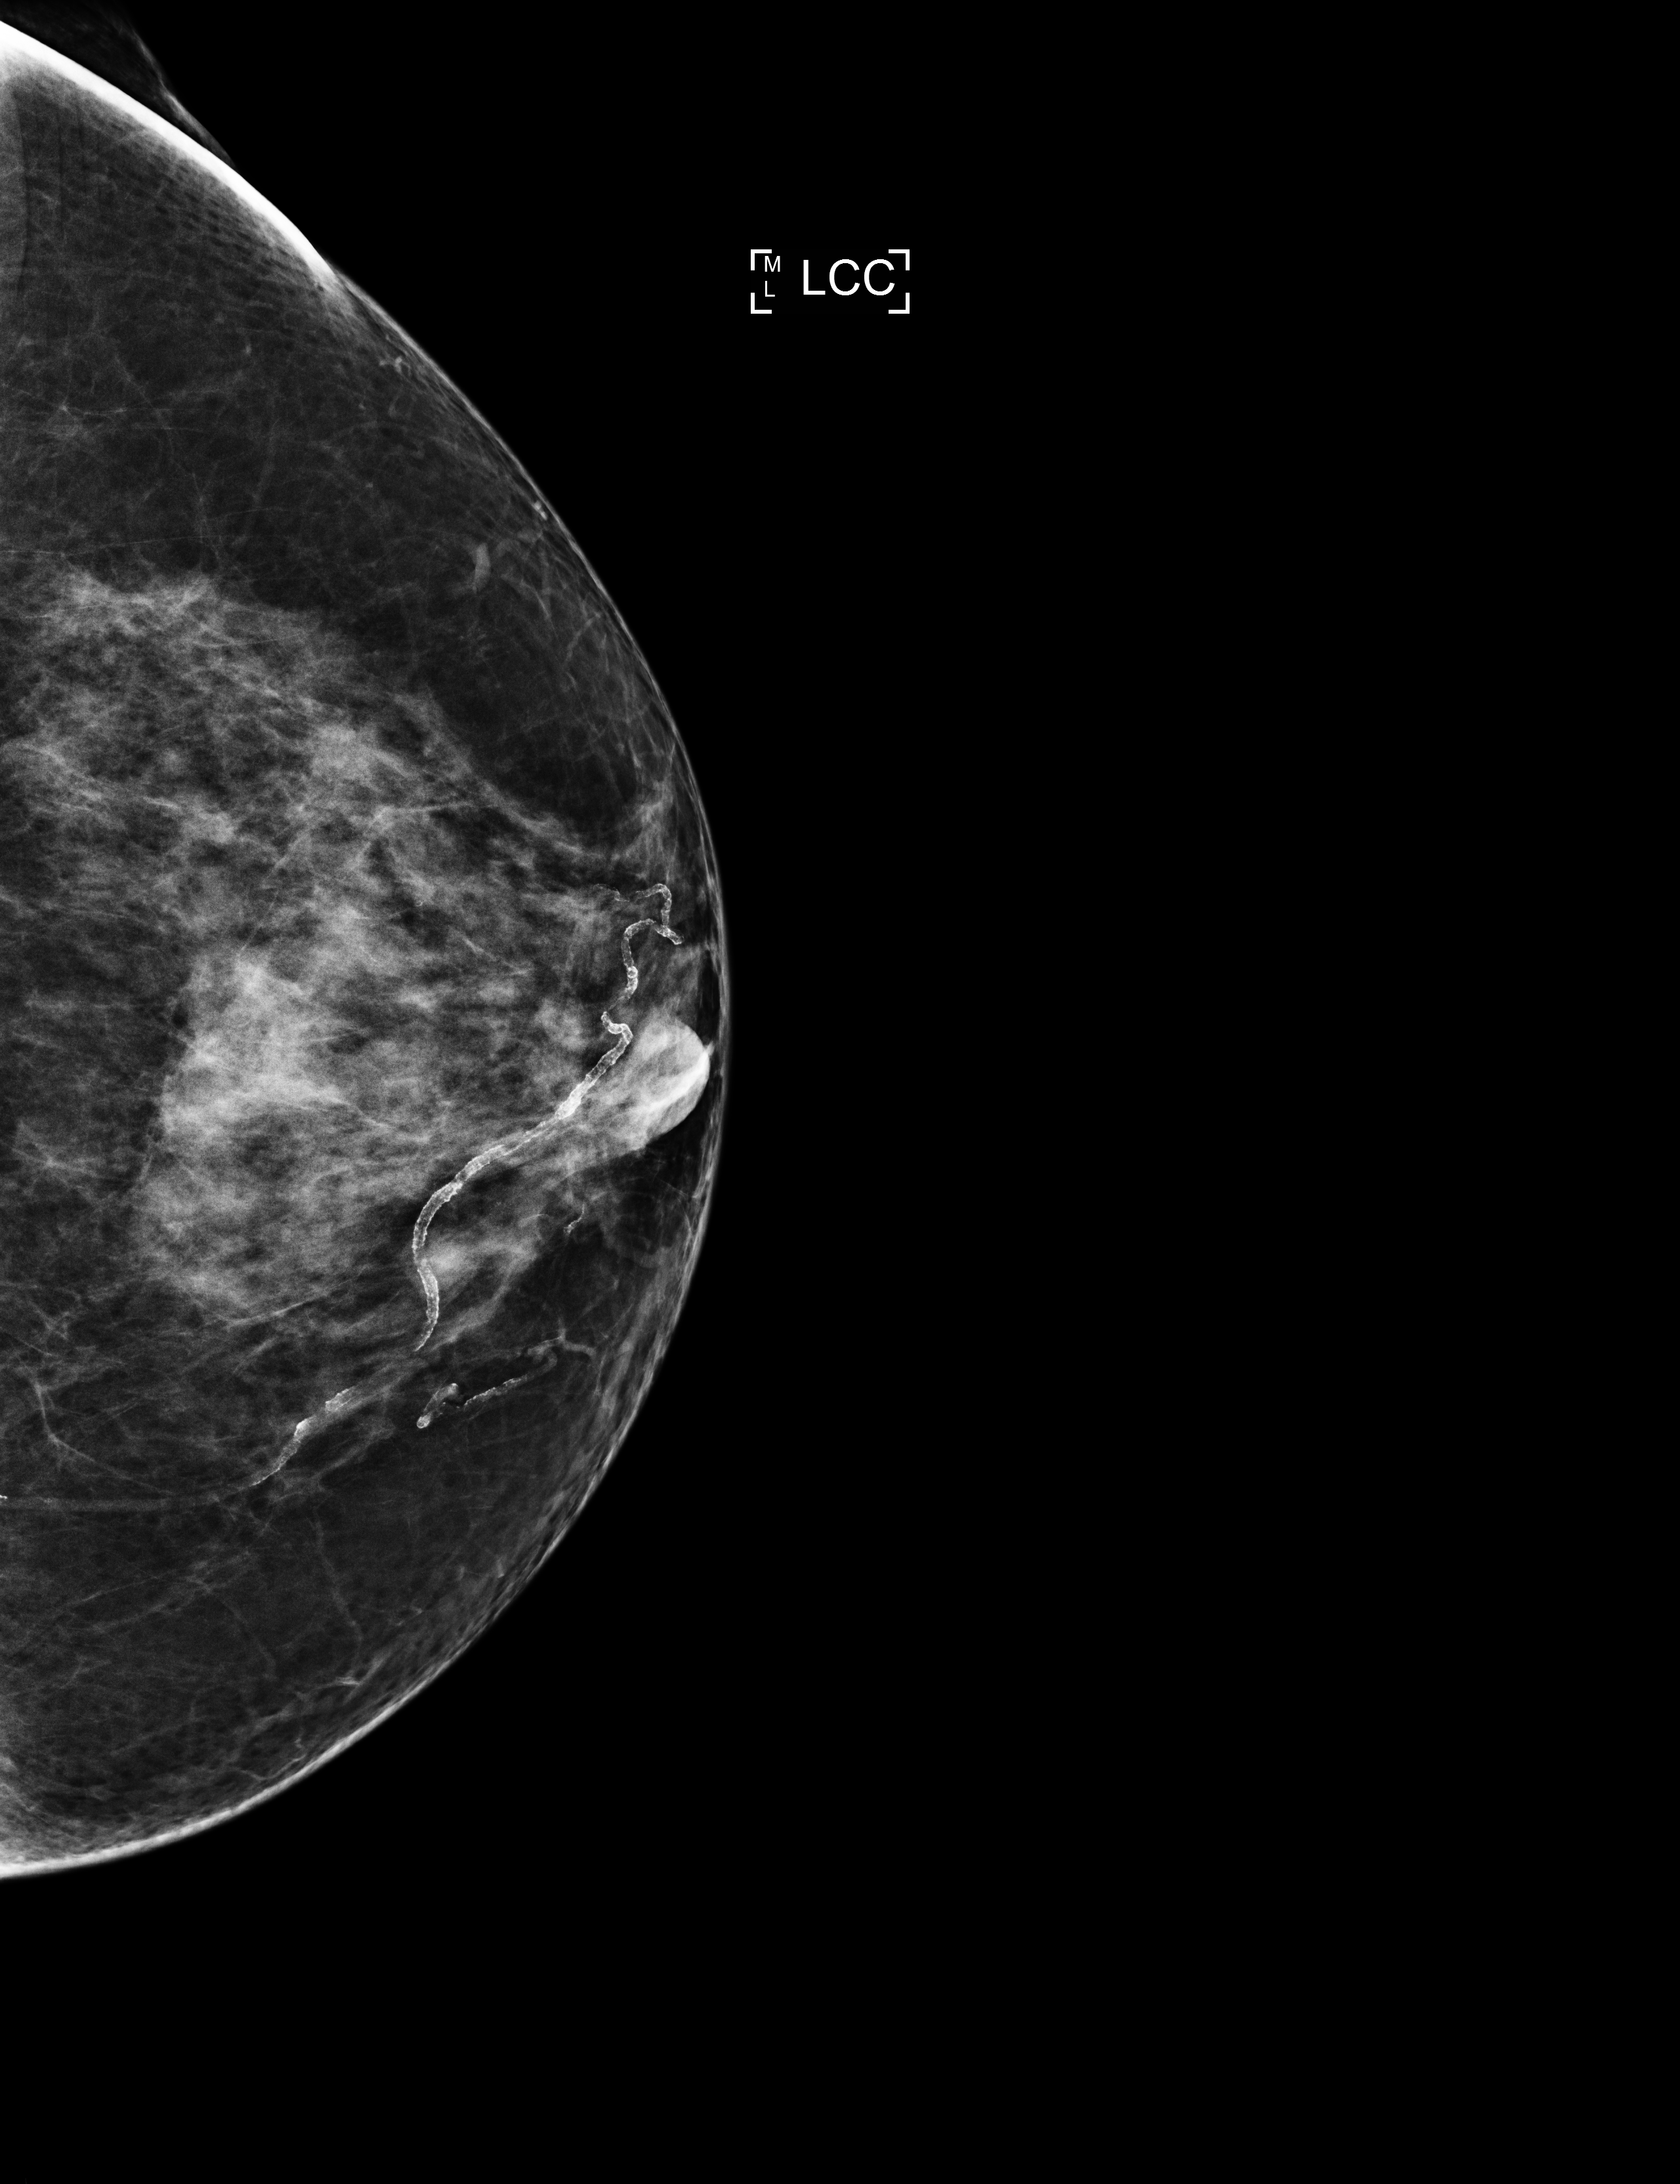
Annual screening mammography examination; compressed breast thickness 62 mm. Patient aged 60 years (female).
Image type: full-field digital mammogram. Breast: left. Projection: cranio-caudal projection.